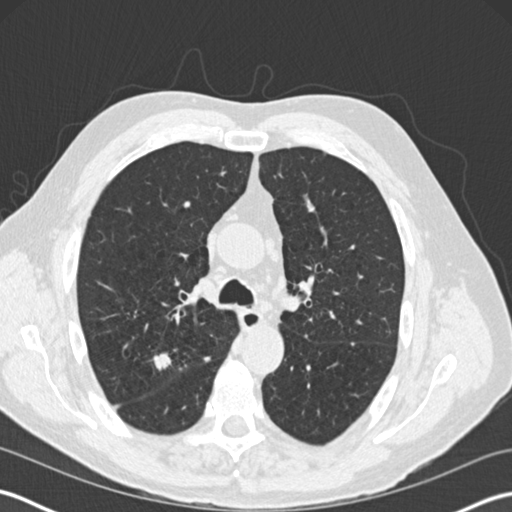
Chest CT (low-dose screening protocol), one axial image. Third screening round (two years after baseline). Lung window (W 1500 / L -600 HU). Standard (soft-tissue) reconstruction kernel (B30f). 120 kVp. Slice 73 of 199 in the series. 512 × 512 image matrix, field of view 350 × 350 mm. Male, age 65 years at enrolment. Former smoker at enrolment.
Expert-annotated lung lesion, bounding box (x1, y1, x2, y2) in pixels: (142, 346, 181, 380). The screening reader recorded 6 non-calcified nodules or masses ≥4 mm on this exam; which of them this box marks is not recorded. Later outcome: lung cancer diagnosed 78 days after this screen — adenocarcinoma, NOS, right upper lobe, moderately differentiated (G2), stage IA (AJCC 6th edition), 16 mm at pathology.